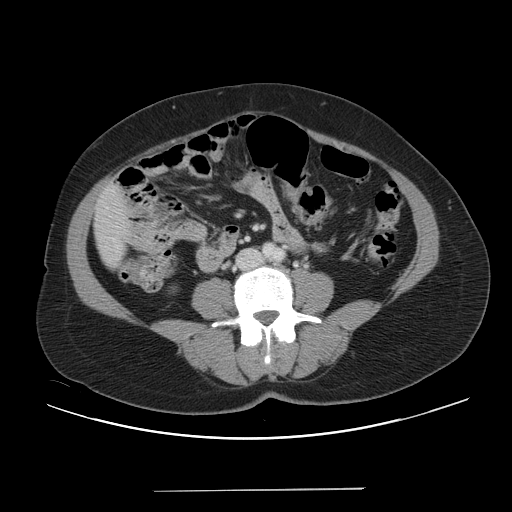
Contrast-enhanced abdominal CT, one axial slice; position 5 of 56 along the scan axis; 120 kVp; intravenous contrast given; soft-tissue window (W 400 / L 40 HU); 5 mm slice thickness; 512 × 512 image matrix. Female patient, age 54 years. Case-level facts recorded for this patient, not image findings: diagnosis: colorectal cancer liver metastases, imaged before liver resection; multiple liver metastases: yes; largest metastasis: 3.2 cm; disease in both lobes: yes.
Structures marked on this image (outlined manually by an expert reader):
- liver: bounding box [x1, y1, x2, y2] px = [95, 185, 129, 267]